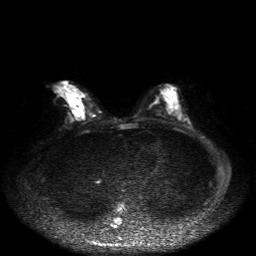
Breast MRI, one axial slice. Position 22 of 50 along the scan axis. Diffusion-weighted series; image 2 of 4 stored at this slice position (different b-values; order by instance number). 1.5 T. 4 mm slice thickness. 256 × 256 image matrix, field of view 360 × 360 mm. Female patient.
Outlined on this slice (expert manual segmentation):
- tumour on diffusion-weighted imaging: bounding box <76,108,82,111> (left, top, right, bottom; pixels)